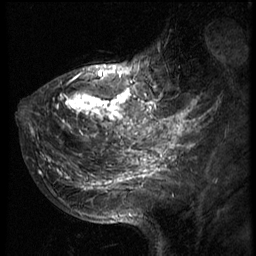
Breast MRI (dynamic contrast-enhanced), one sagittal slice; slice 23 of 66 in the series (ordered by position); 3 images stored at this slice position (order not interpretable as contrast timing); 1.5 T; TE 4.2 ms, TR 8.9 ms; 2.5 mm slice thickness; 256 × 256 image matrix, field of view 200 × 200 mm. Patient: female, 39 years. Case-level facts recorded for this patient, not image findings: setting: breast cancer imaged before/during neoadjuvant chemotherapy; receptor status: HER2-positive.
Annotated regions visible in this slice (semi-automatic segmentation, software-assisted and operator-edited):
- analysis volume of interest (the breast-tissue region the enhancement analysis was run in; not a lesion): box from (x=29, y=44) to (x=166, y=196) px
- tumour enhancement mask (voxels above the 140 % enhancement threshold inside the analysis volume of interest): (x=31, y=70)–(x=166, y=188)